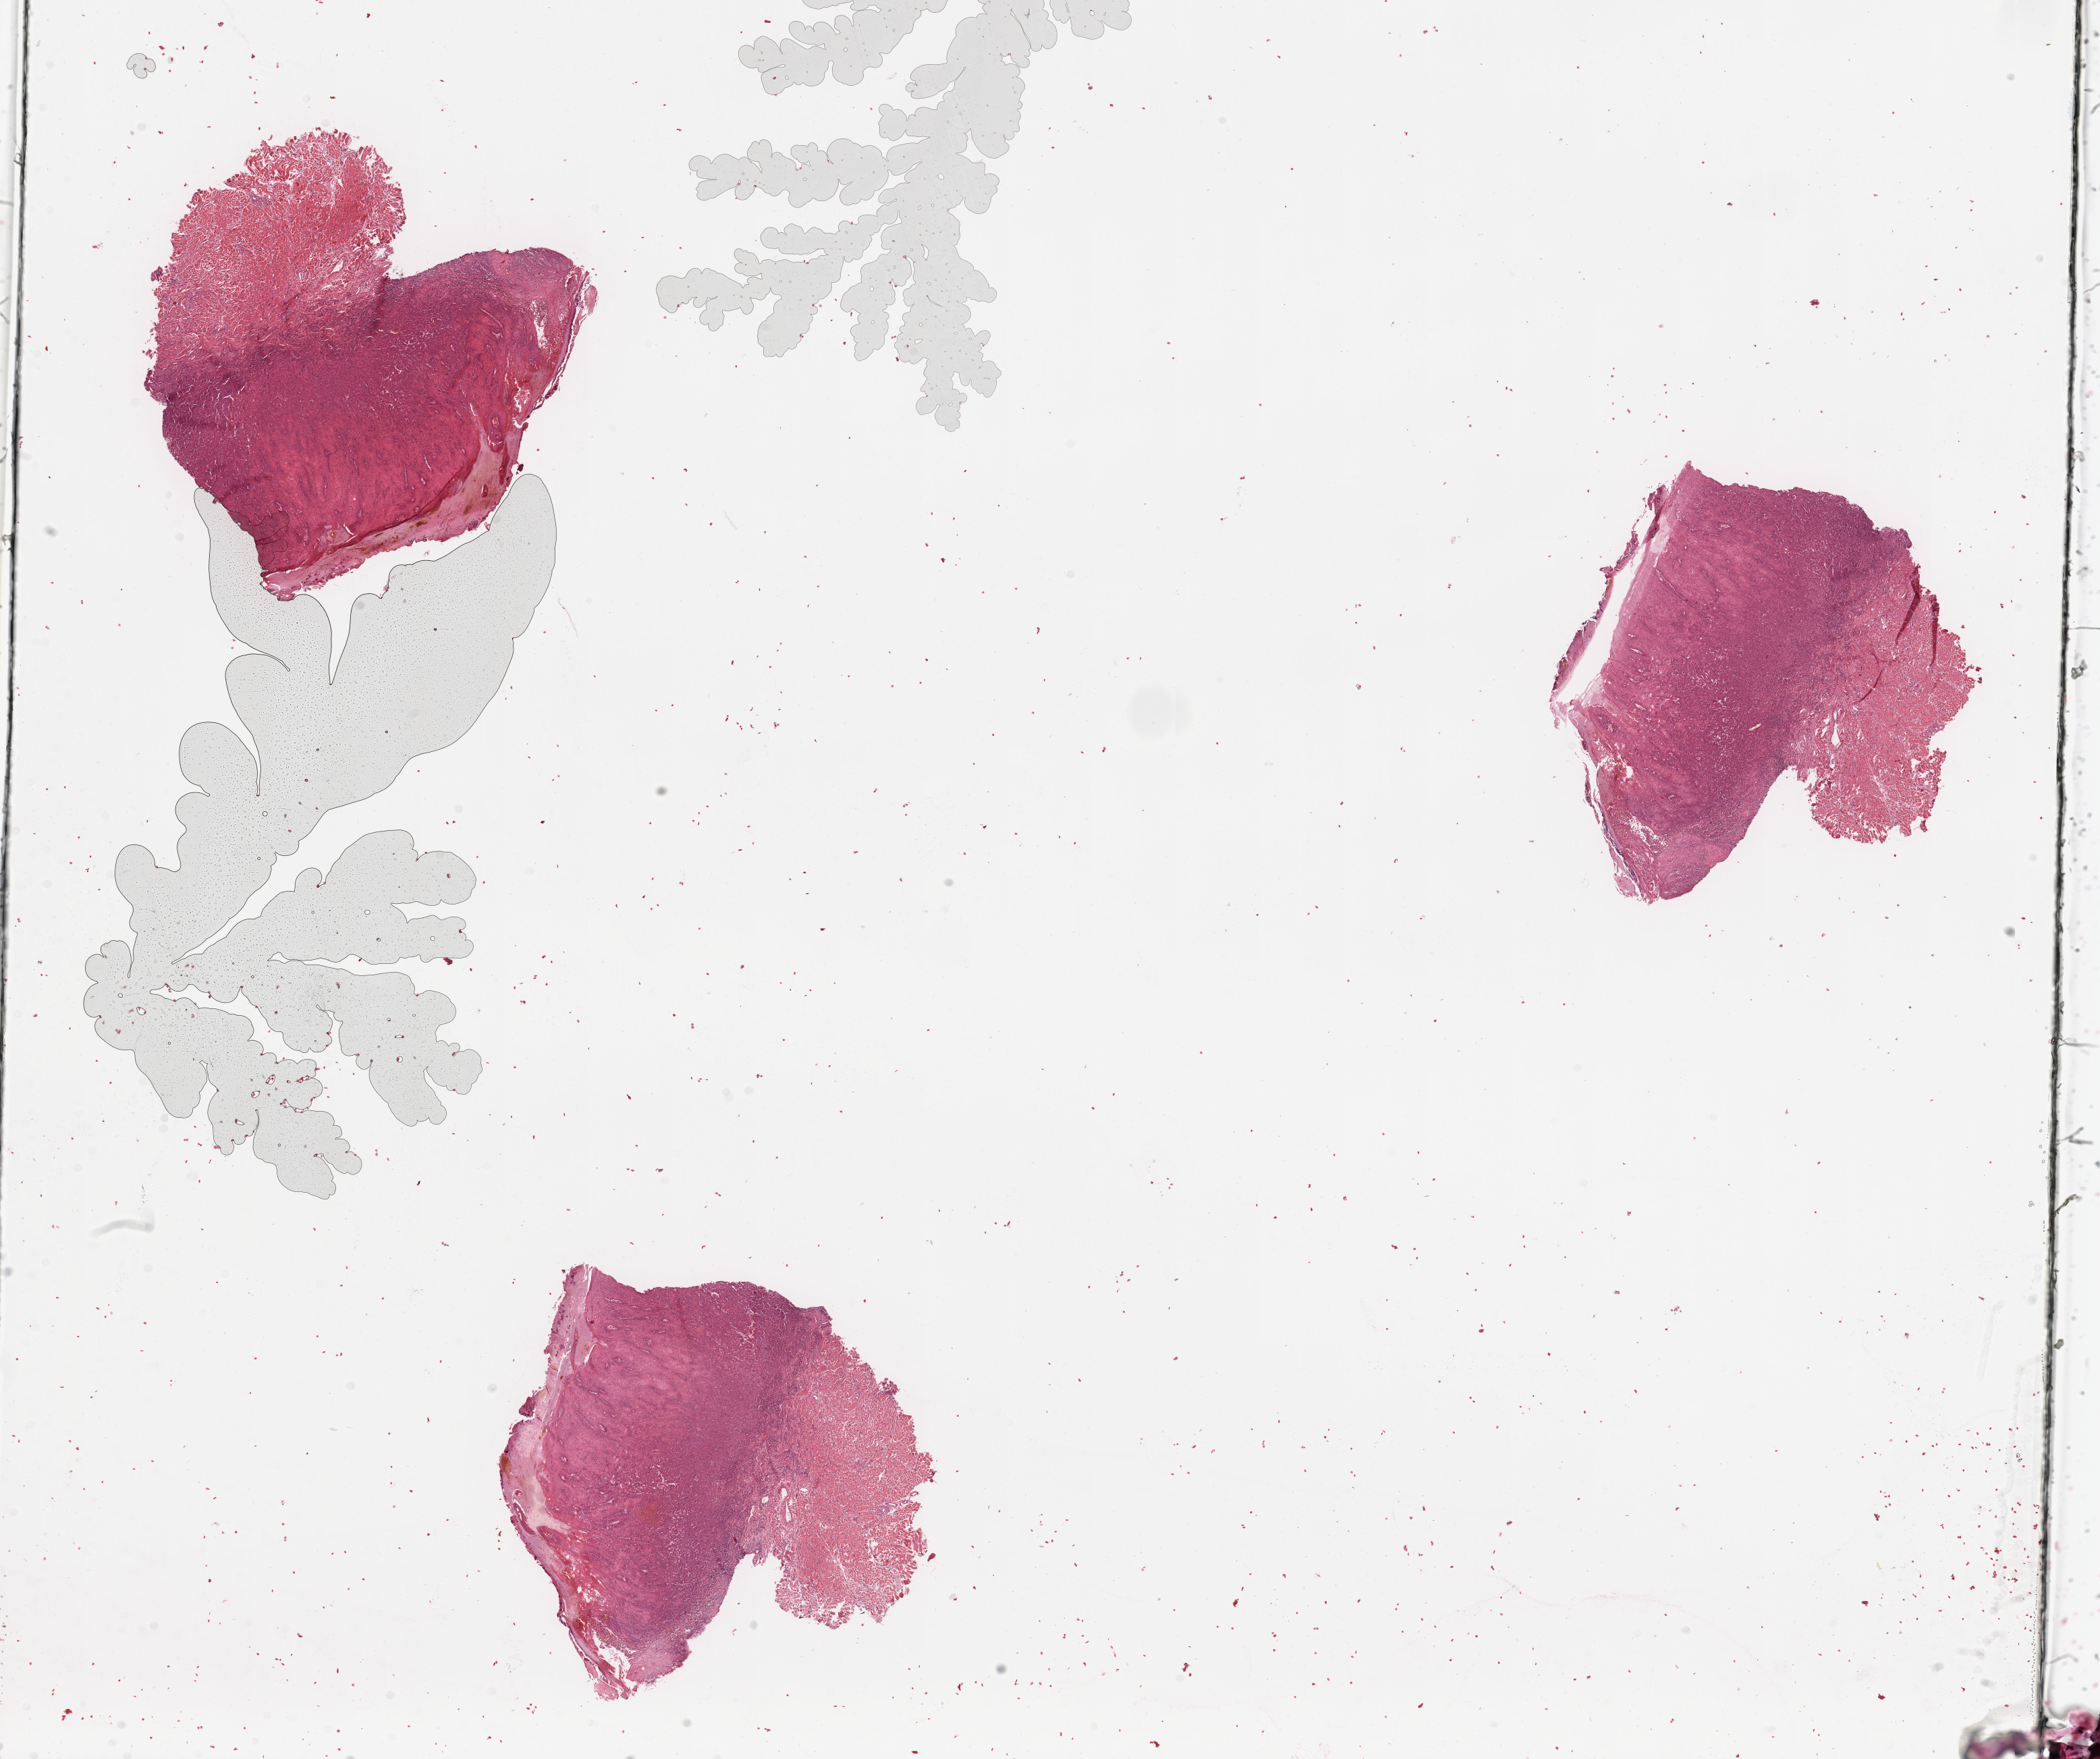
Digitized H&E tissue section (whole slide), low-resolution overview of the scanned area, about 24.6 x 20.6 mm (acquisition: 20x scan), head and neck, tissue type not recorded. Male, 76 y/o.
Patient diagnosis: Squamous cell carcinoma, NOS.